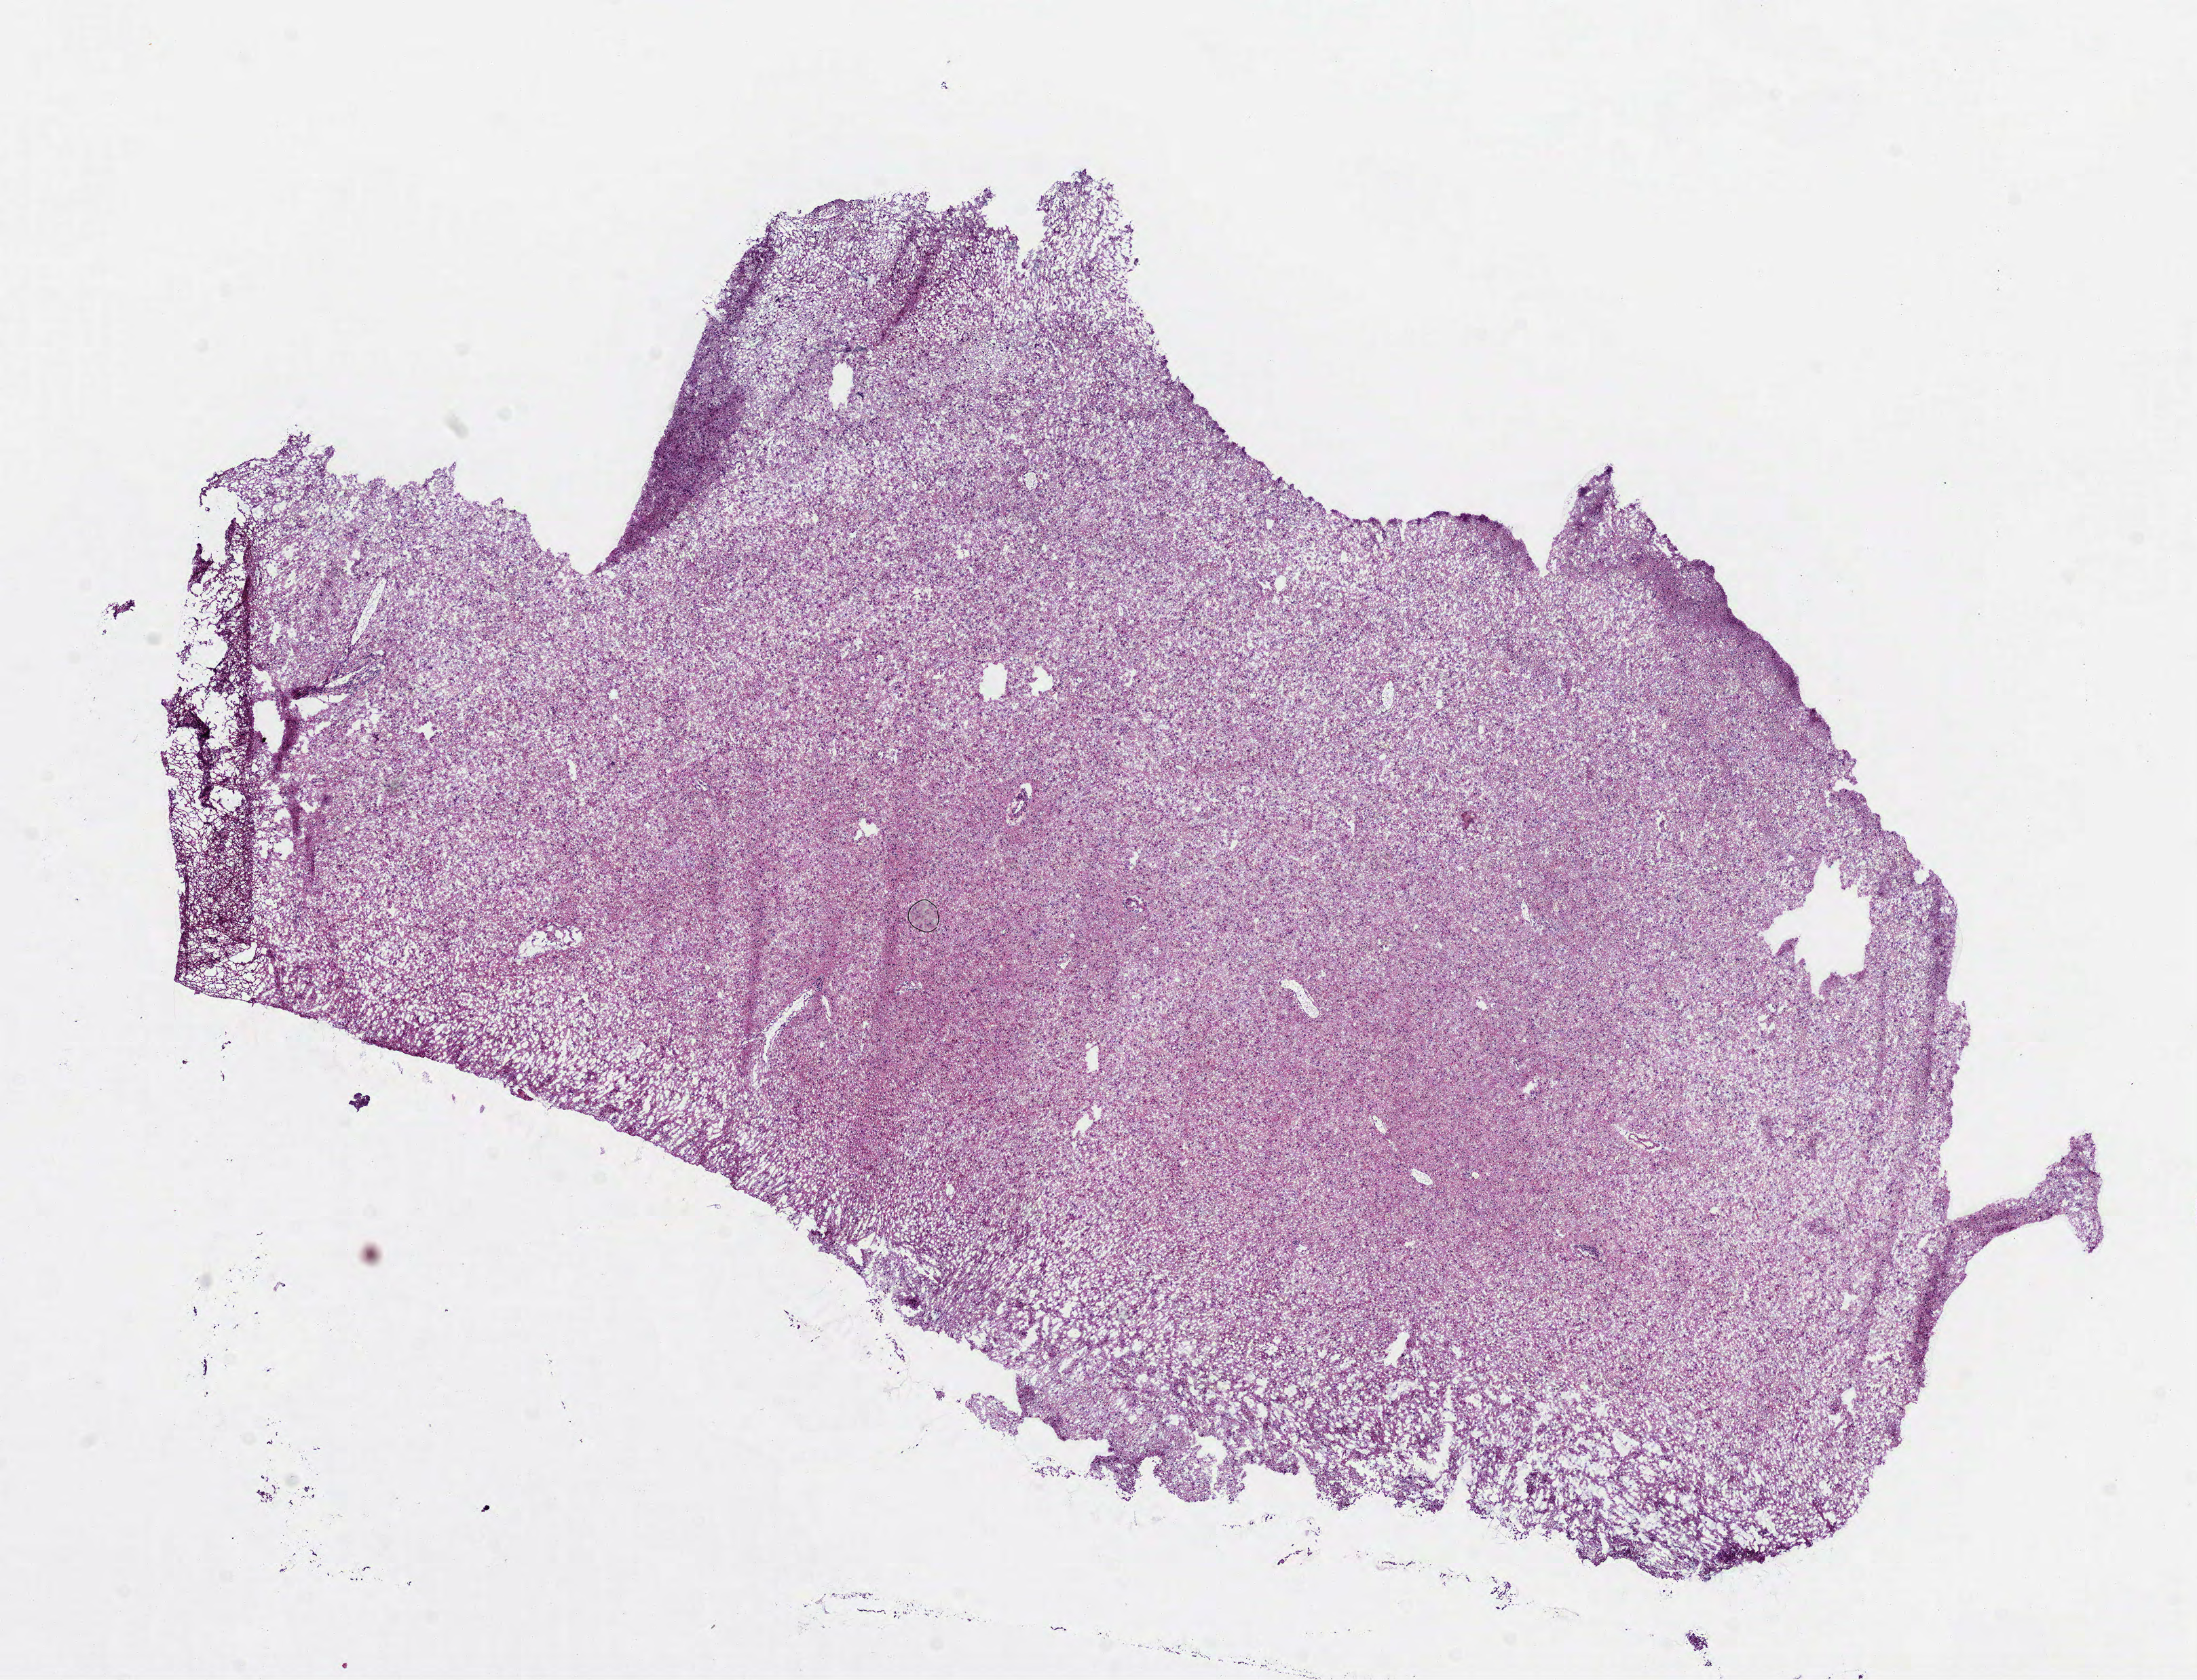
Whole-slide histology image, Hematoxylin and eosin (H&E) stained, a low-resolution overview of the entire scanned area, about 13.1 x 10.0 mm (slide scanned at 40x), frozen section from the bottom of the tissue portion, primary tumour sample from the brain. Male patient; age at initial diagnosis 28 years.
Histologic diagnosis: Astrocytoma, NOS.